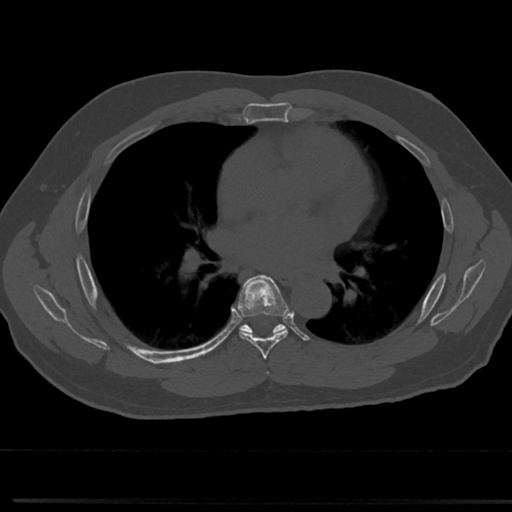
CT including the spine, one axial slice. Position 438 of 817 along the scan axis. Reconstruction kernel Br40s/3. Bone window (W 1800 / L 400 HU). 0.5 mm slice thickness. 512 × 512 image matrix, field of view 355 × 355 mm. Patient: male, 61 years. Case-level facts recorded for this patient, not image findings: primary cancer: prostate.
Outlined on this slice (semi-automatically segmented with operator editing):
- T5 vertebra: bounding box [x1, y1, x2, y2] px = [264, 361, 273, 377]
- T6 vertebra: [230, 277, 308, 351]